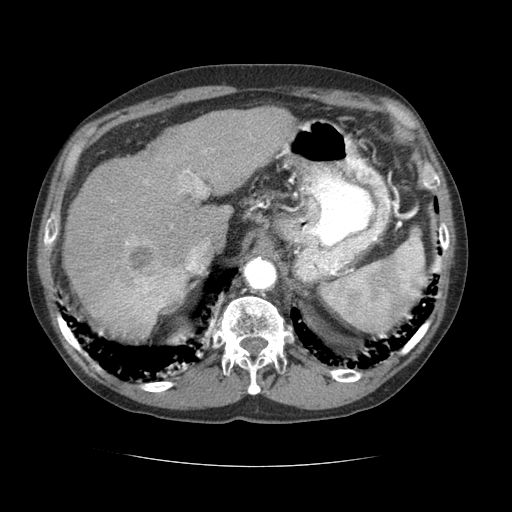
Contrast-enhanced abdominal CT (liver protocol), one axial slice; position 50 of 69 along the scan axis; reconstruction kernel STANDARD; 120 kVp; soft-tissue window (W 400 / L 40 HU); 512 × 512 image matrix, field of view 360 × 360 mm. Case-level facts recorded for this patient, not image findings: diagnosis: hepatocellular carcinoma (patient treated with transarterial chemoembolisation; whether this scan precedes or follows treatment is not stated here); TNM stage (as recorded): Stage-II; Child-Pugh class: B; tumour differentiation: poorly differentiated; tumour size: 2.6 cm.
Structures marked on this image (semi-automatically segmented with operator editing):
- liver parenchyma outside the tumour (the mass and vessels are separate outlines, so this box may not span the whole liver): bounding box (x1, y1, x2, y2) in pixels: (62, 106, 294, 323)
- mass: (95, 235, 186, 338)
- liver vessels: (179, 169, 207, 271)